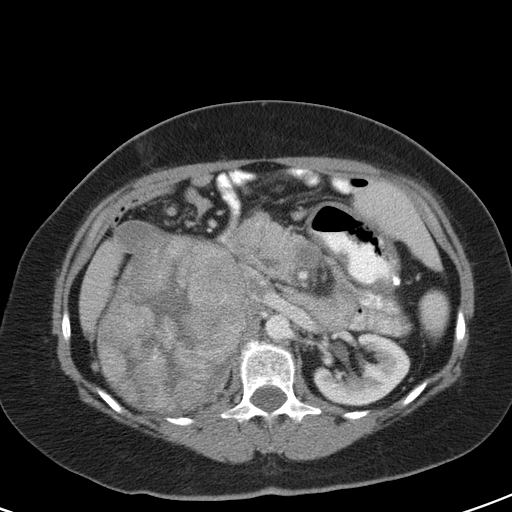
Contrast-enhanced abdominal CT, one axial slice; slice 66 of 126 in the series (ordered by position); intravenous contrast given; soft-tissue window (W 400 / L 40 HU); 5 mm slice thickness; 512 × 512 image matrix, field of view 356 × 356 mm. Female patient, age 51 years. Case-level facts recorded for this patient, not image findings: diagnosis: adrenocortical carcinoma; tumour side: right adrenal; tumour size at pathology: 17 cm; Ki-67 index: 12 %; stage (as recorded): 2.
Annotated regions visible in this slice (semi-automatically segmented with operator editing):
- mass: bounding box <96,224,244,409> (left, top, right, bottom; pixels)